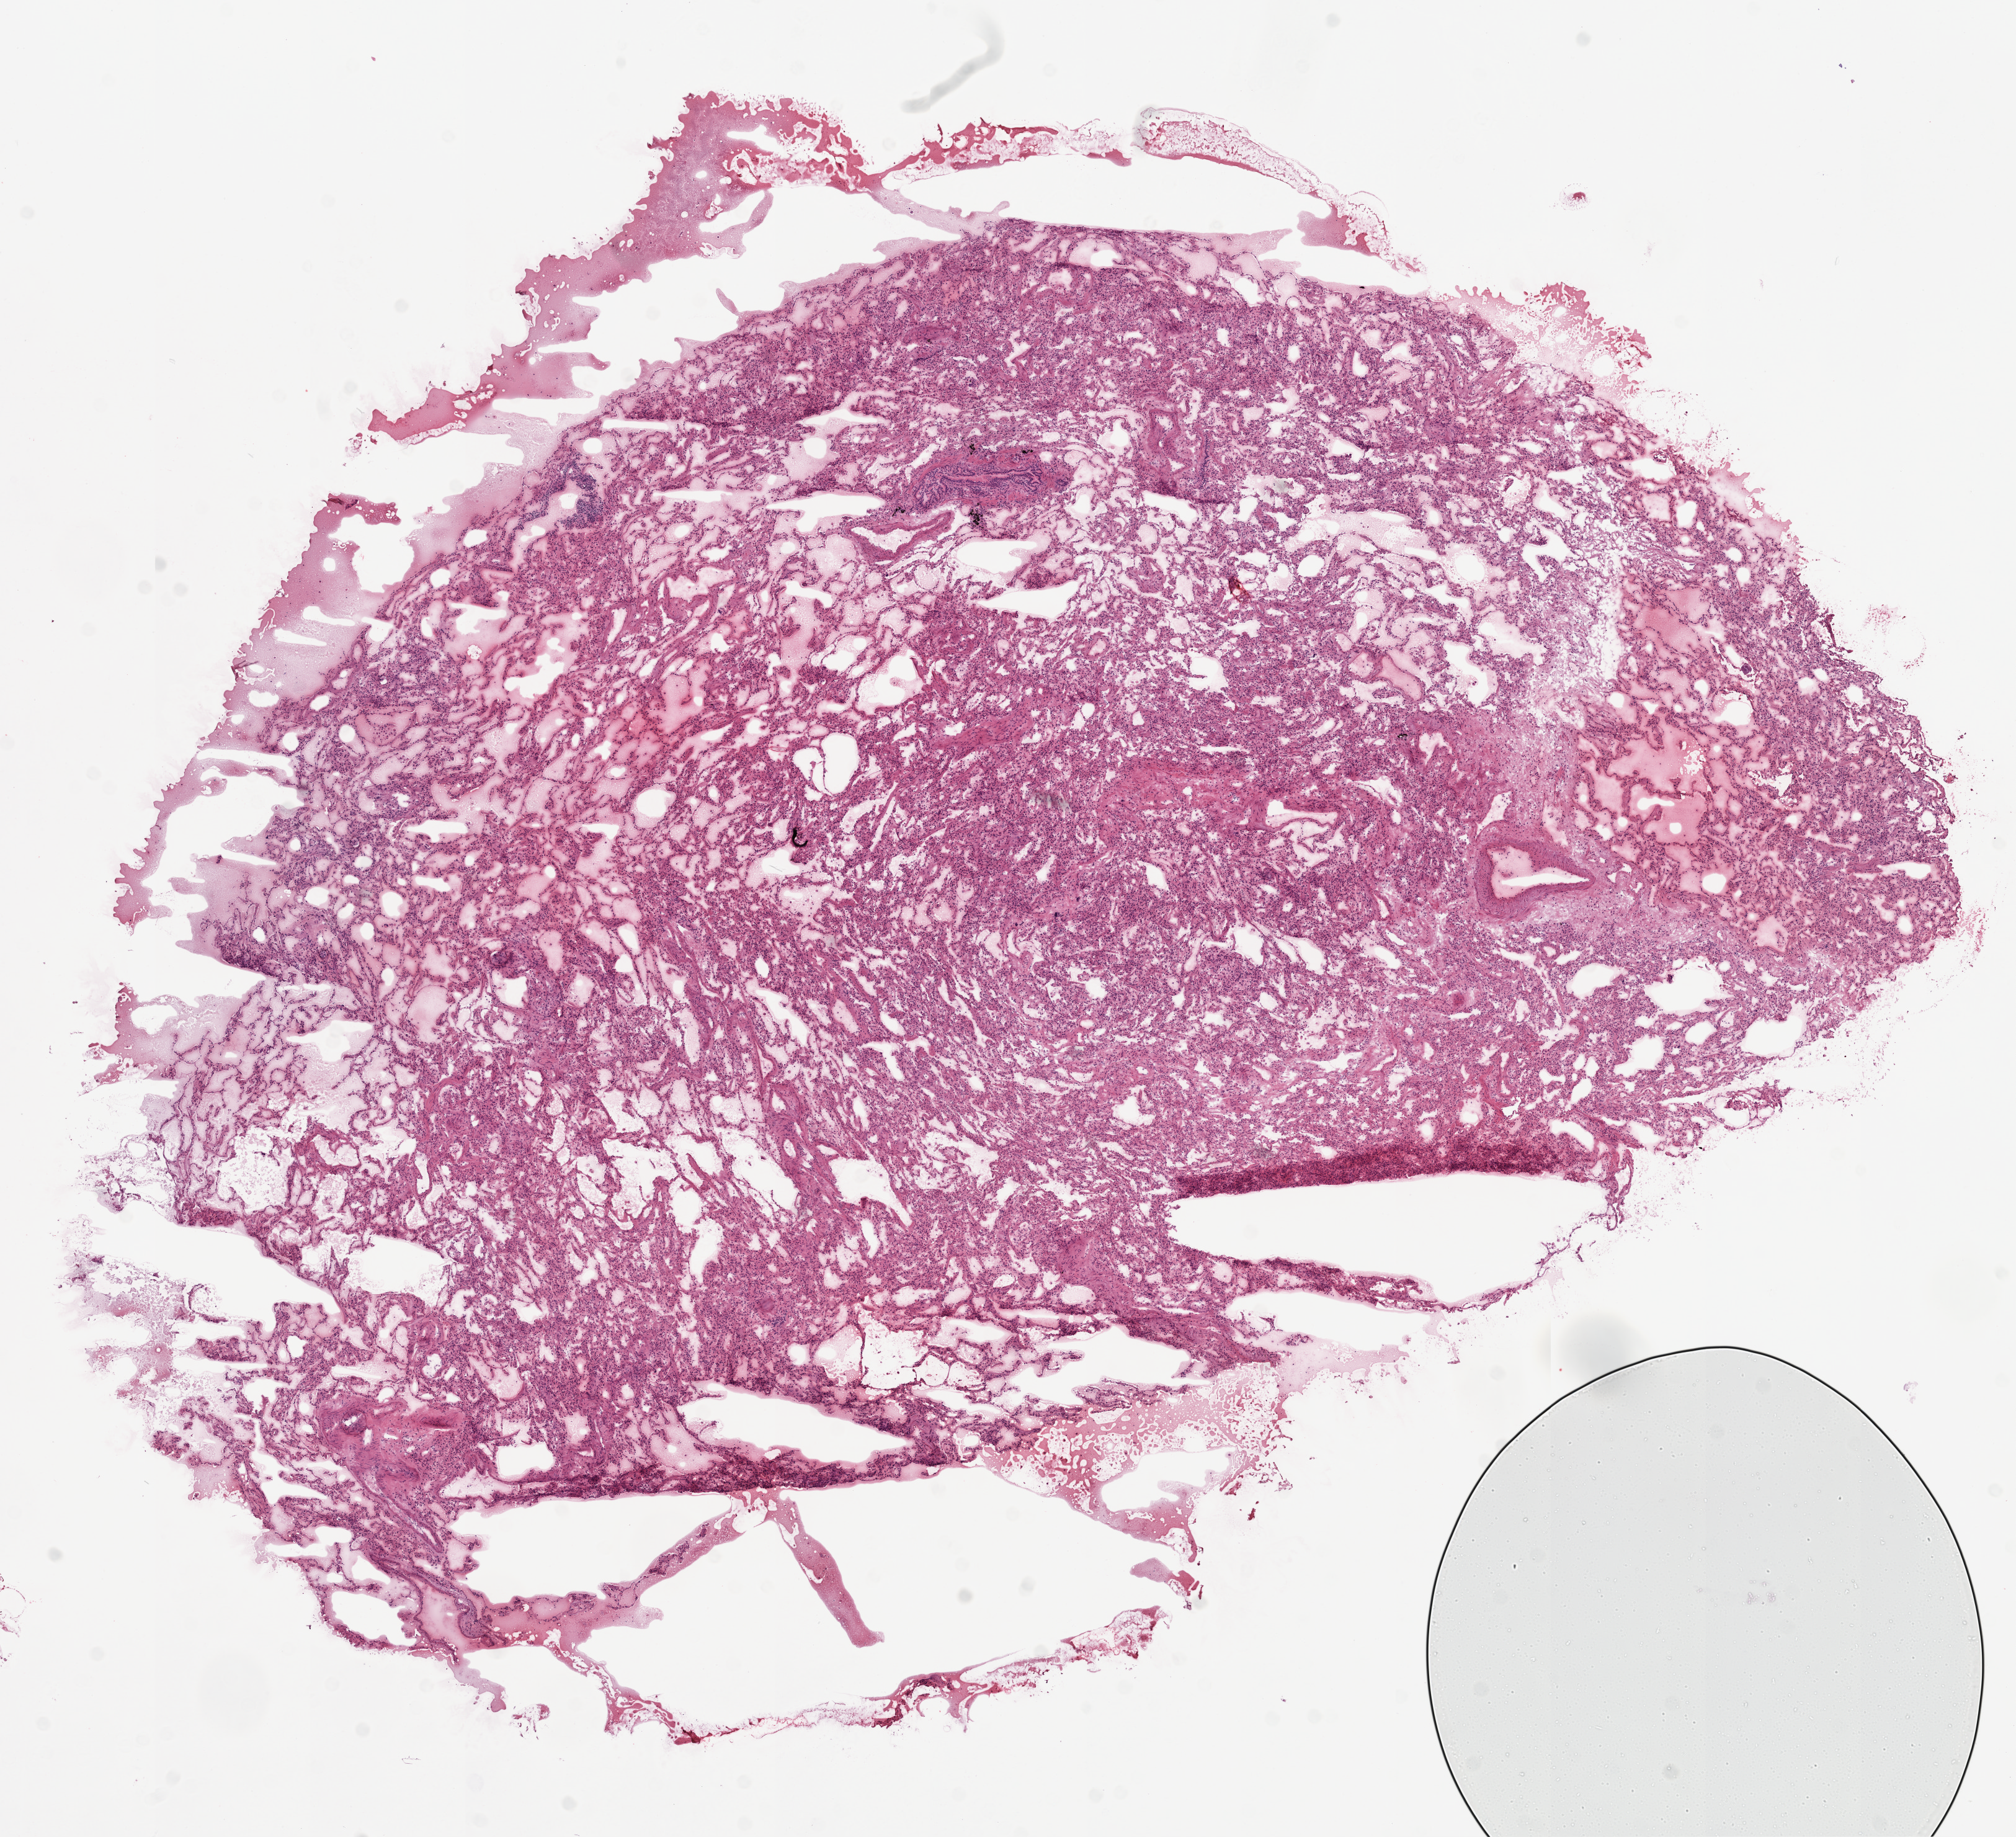
H&E whole-slide image — low-resolution overview of the scanned area, about 13.0 x 11.9 mm (from a 20x scan), frozen section from the top of the tissue portion, lung, solid tissue normal (non-tumour tissue) sample. Female patient; age at initial diagnosis 67 years.
* this section: solid tissue normal (non-tumour) sample from the same patient
* patient diagnosis: Adenocarcinoma, NOS